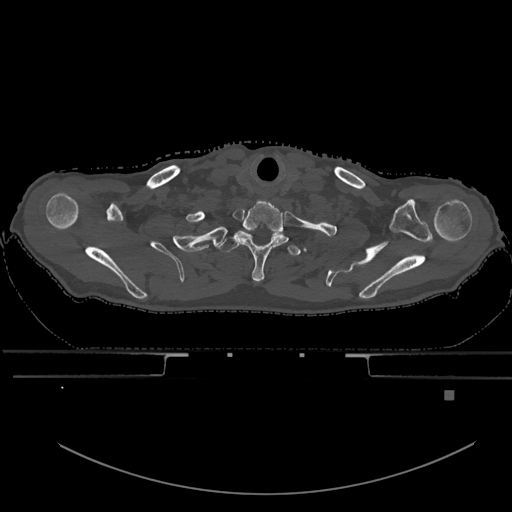
CT including the spine, one axial slice; slice 563 of 969 in the series (ordered by position); bone window (W 1800 / L 400 HU); 0.5 mm slice thickness; 512 × 512 image matrix. Male patient, age 82 years. From the clinical record (not read from this slice): primary cancer: prostate.
Outlined on this slice (semi-automatic segmentation, software-assisted and operator-edited):
- T1 vertebra: bounding box <218,236,301,257> (left, top, right, bottom; pixels)